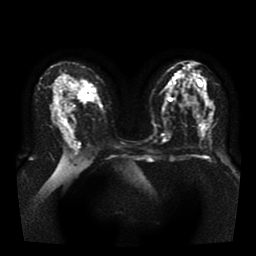
Breast MRI, one axial slice. Slice 22 of 41 in the series (ordered by position). Diffusion-weighted series; image 2 of 4 stored at this slice position (different b-values; order by instance number). 1.5 T. 5 mm slice thickness. 256 × 256 image matrix. Female patient.
Structures marked on this image (expert manual segmentation):
- tumour on diffusion-weighted imaging: bounding box <79,86,95,104> (left, top, right, bottom; pixels)